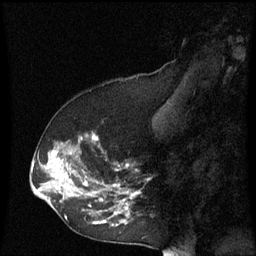
Breast MRI (dynamic contrast-enhanced), one sagittal slice. Slice 26 of 60 in the series (ordered by position). Dynamic contrast-enhanced series, image 2 of 3 at this slice position (ordered by acquisition). 1.5 T. TE 4.2 ms, TR 8.9 ms. 256 × 256 image matrix, field of view 200 × 200 mm. Female patient, age 53 years. From the clinical record (not read from this slice): setting: breast cancer imaged before/during neoadjuvant chemotherapy; receptor status: HR-positive, HER2-negative.
Structures marked on this image (semi-automatic segmentation, software-assisted and operator-edited):
- analysis volume of interest (the breast-tissue region the enhancement analysis was run in; not a lesion): bounding box <38,134,141,227> (left, top, right, bottom; pixels)
- tumour enhancement mask (voxels above the 70 % enhancement threshold inside the analysis volume of interest): <48,150,139,223>